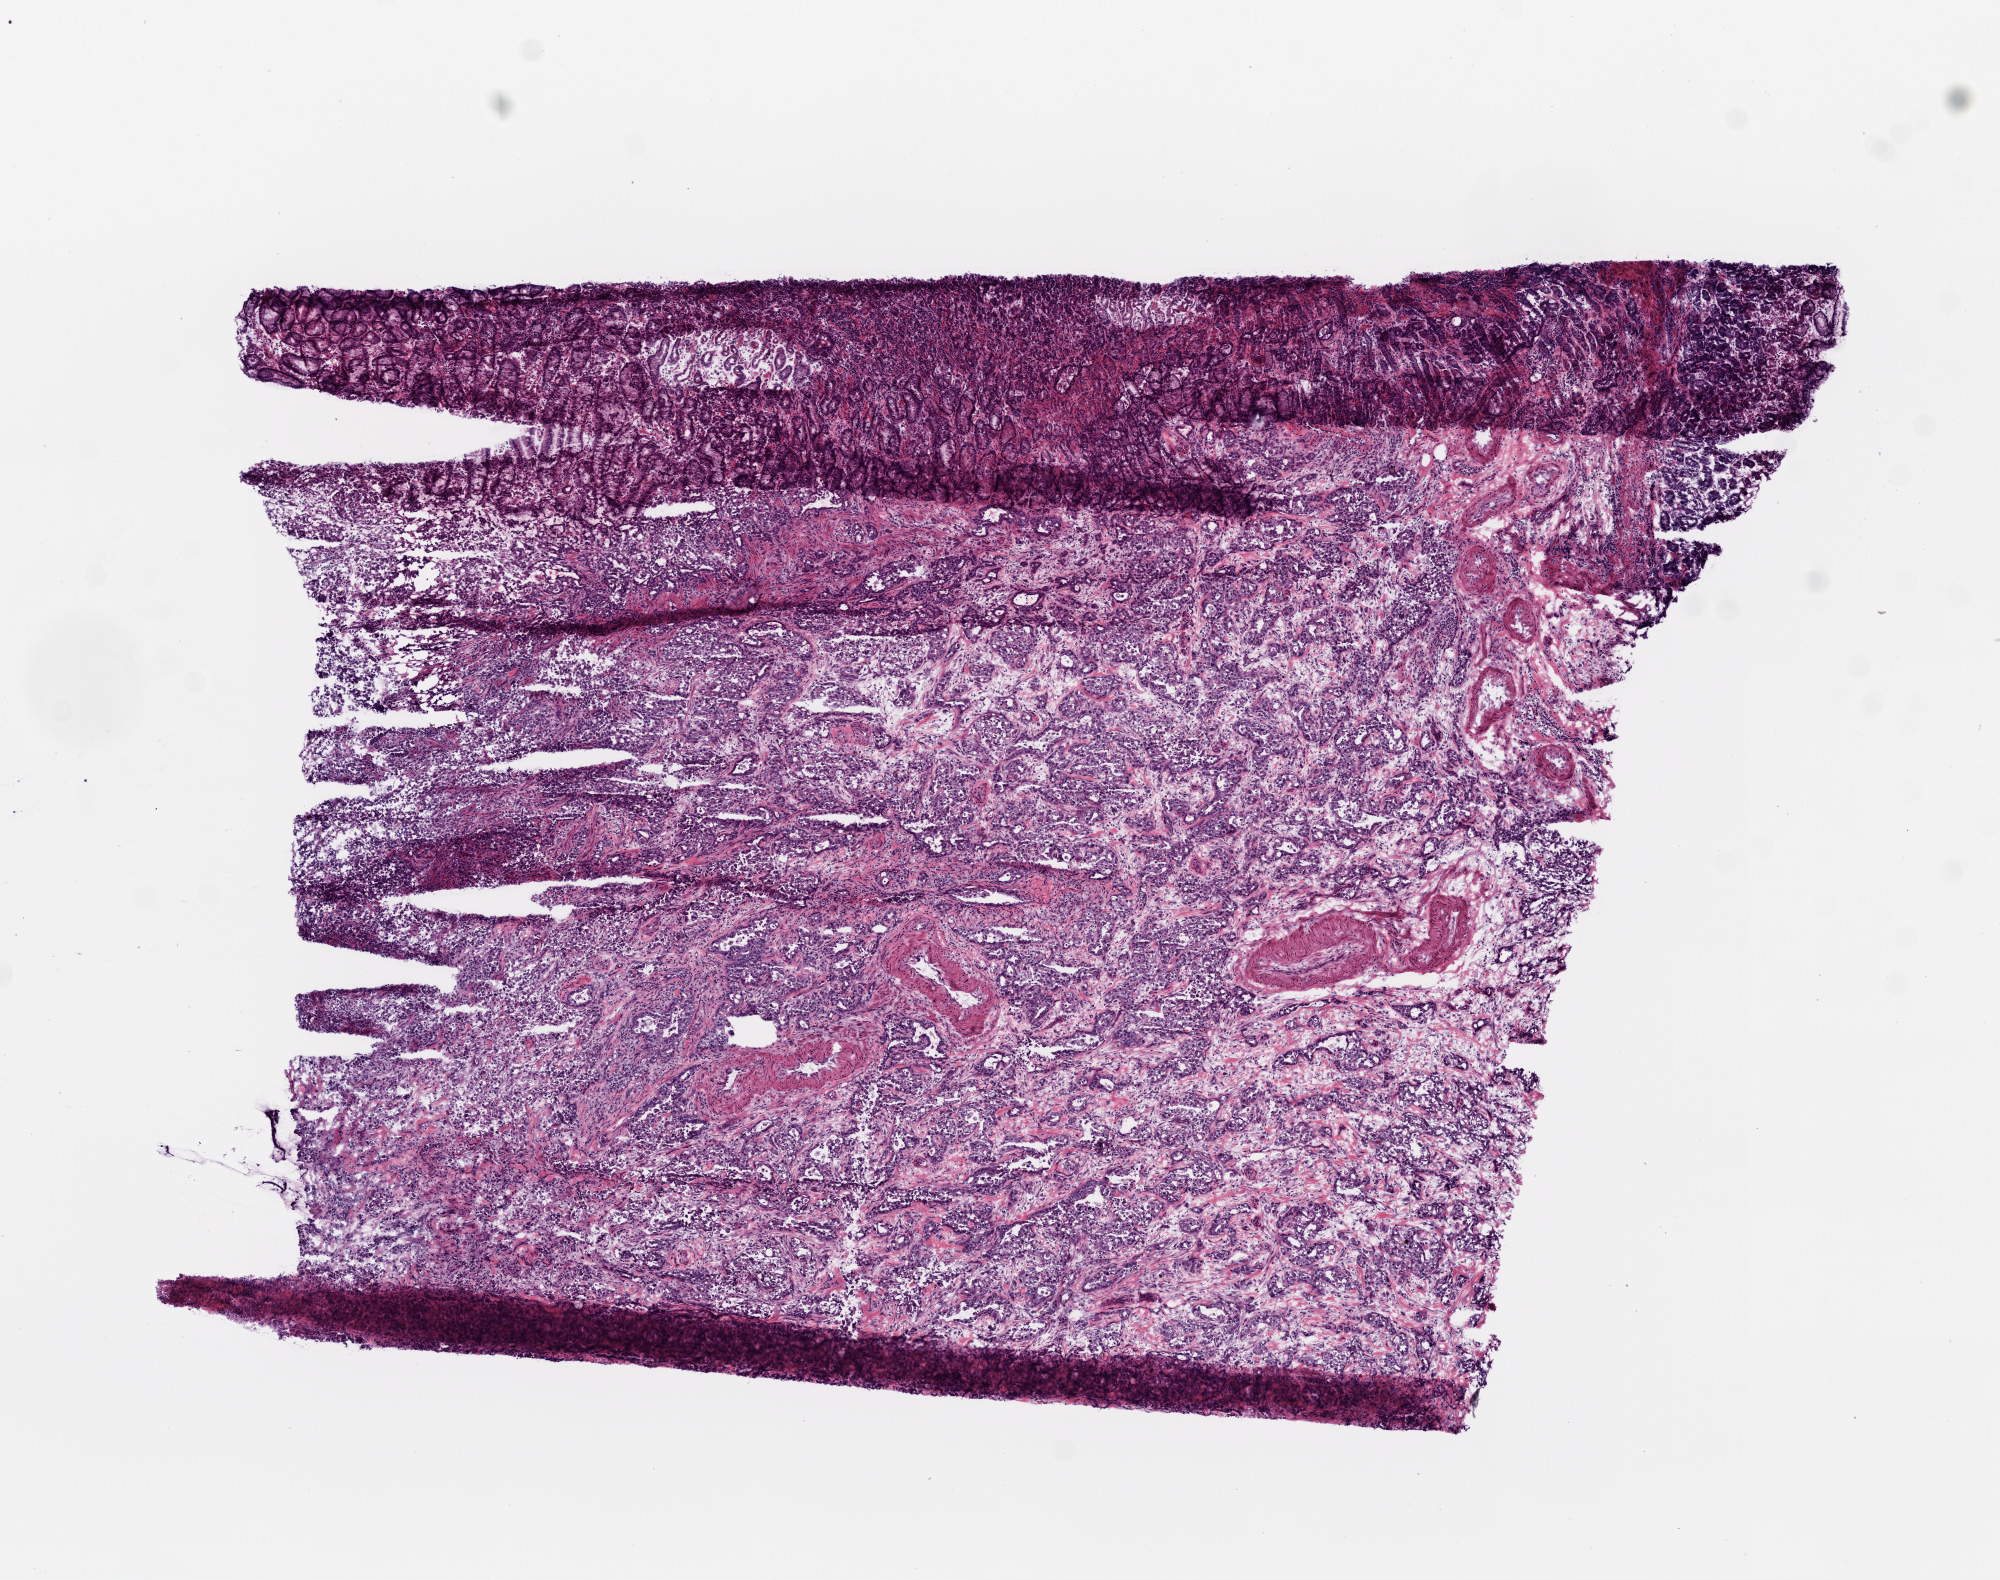
Whole-slide histology image, Hematoxylin and eosin (H&E) stained, shown as a low-resolution overview of the whole scanned area (about 8.0 x 6.3 mm, slide scanned at 20x), frozen section from the bottom of the tissue portion, sample: primary tumour, stomach. Female patient; age at initial diagnosis 75 years. Histologic grade: G3 (poorly differentiated). Composition of this section per pathologist review: tumour cells 75%, tumour nuclei 74%, normal cells 19%, stromal cells 6%, necrosis 0%. Infiltration values recorded for this section: lymphocyte infiltration 5%, monocyte infiltration 0%, neutrophil infiltration 7%.
- diagnosis: Adenocarcinoma, NOS (cardia, NOS)
- lymph nodes positive (case pathology): 6 of 18 examined
- AJCC pathologic stage: IV